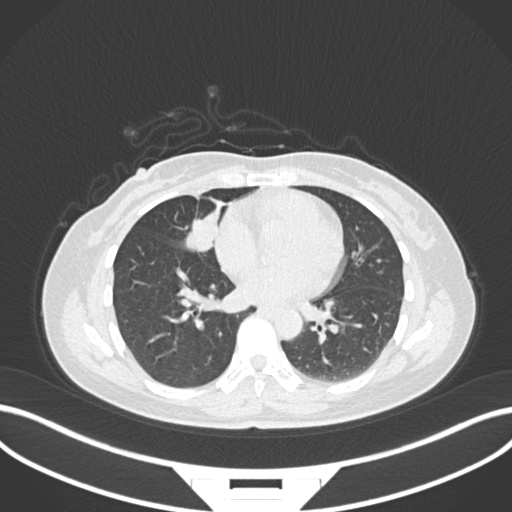
Chest CT, one axial slice; slice 67 of 171 in the series (ordered by position); 120 kVp; lung window (W 1500 / L -600 HU); 1 mm slice thickness; 512 × 512 image matrix, field of view 400 × 400 mm. Female patient, age 43 years. From the clinical record (not read from this slice): clinical TNM (as recorded): T1c N3 M1; histopathological grade: G1.
Structures marked on this image (bounding box drawn by a radiologist):
- lung tumour (recorded histology: adenocarcinoma): bounding box (x1, y1, x2, y2) in pixels: (184, 209, 223, 257)